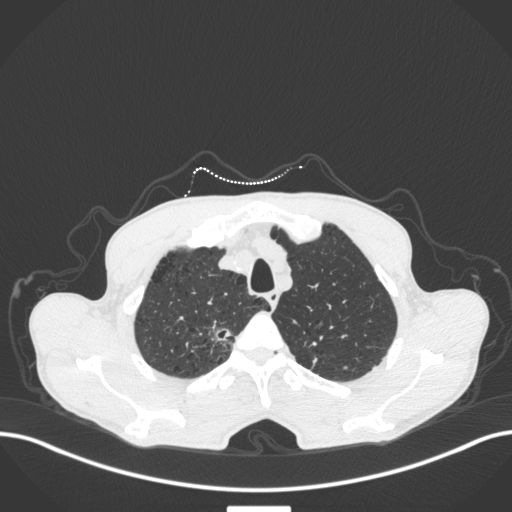
Chest CT, one axial slice; slice 364 of 445 in the series (ordered by position); lung window (W 1500 / L -600 HU); 512 × 512 image matrix, field of view 400 × 400 mm. Male patient, age 70 years. Case-level facts recorded for this patient, not image findings: clinical TNM (as recorded): T1a N0 M0; histopathological grade: G1-2.
Outlined on this slice (rectangle marked by the reading radiologist):
- lung tumour (recorded histology: adenocarcinoma): bounding box <206,316,234,348> (left, top, right, bottom; pixels)